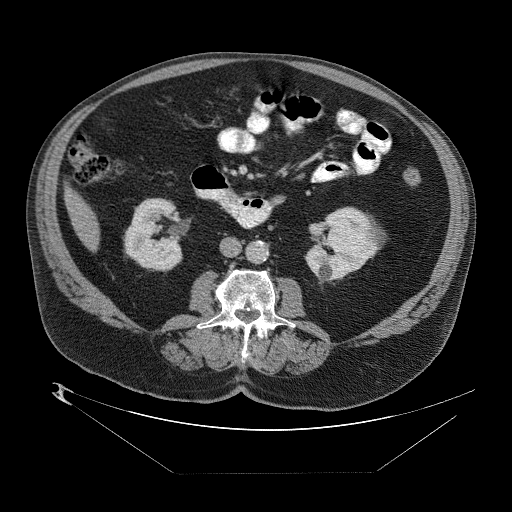
Contrast-enhanced abdominal CT (liver protocol), one axial slice; slice 7 of 89 in the series (ordered by position); one of 2 acquisitions stored at this slice position; soft-tissue window (W 400 / L 40 HU); 2.5 mm slice thickness; 512 × 512 image matrix, field of view 480 × 480 mm. Case-level facts recorded for this patient, not image findings: diagnosis: hepatocellular carcinoma (patient treated with transarterial chemoembolisation; whether this scan precedes or follows treatment is not stated here); TNM stage (as recorded): Stage-II; Child-Pugh class: B; tumour differentiation: moderately differentiated; tumour nodularity: multinodular.
Annotated regions visible in this slice (semi-automatically segmented with operator editing):
- abdominal aorta: bounding box <247,241,269,265> (left, top, right, bottom; pixels)
- liver parenchyma outside the tumour (the mass and vessels are separate outlines, so this box may not span the whole liver): <62,177,96,238>